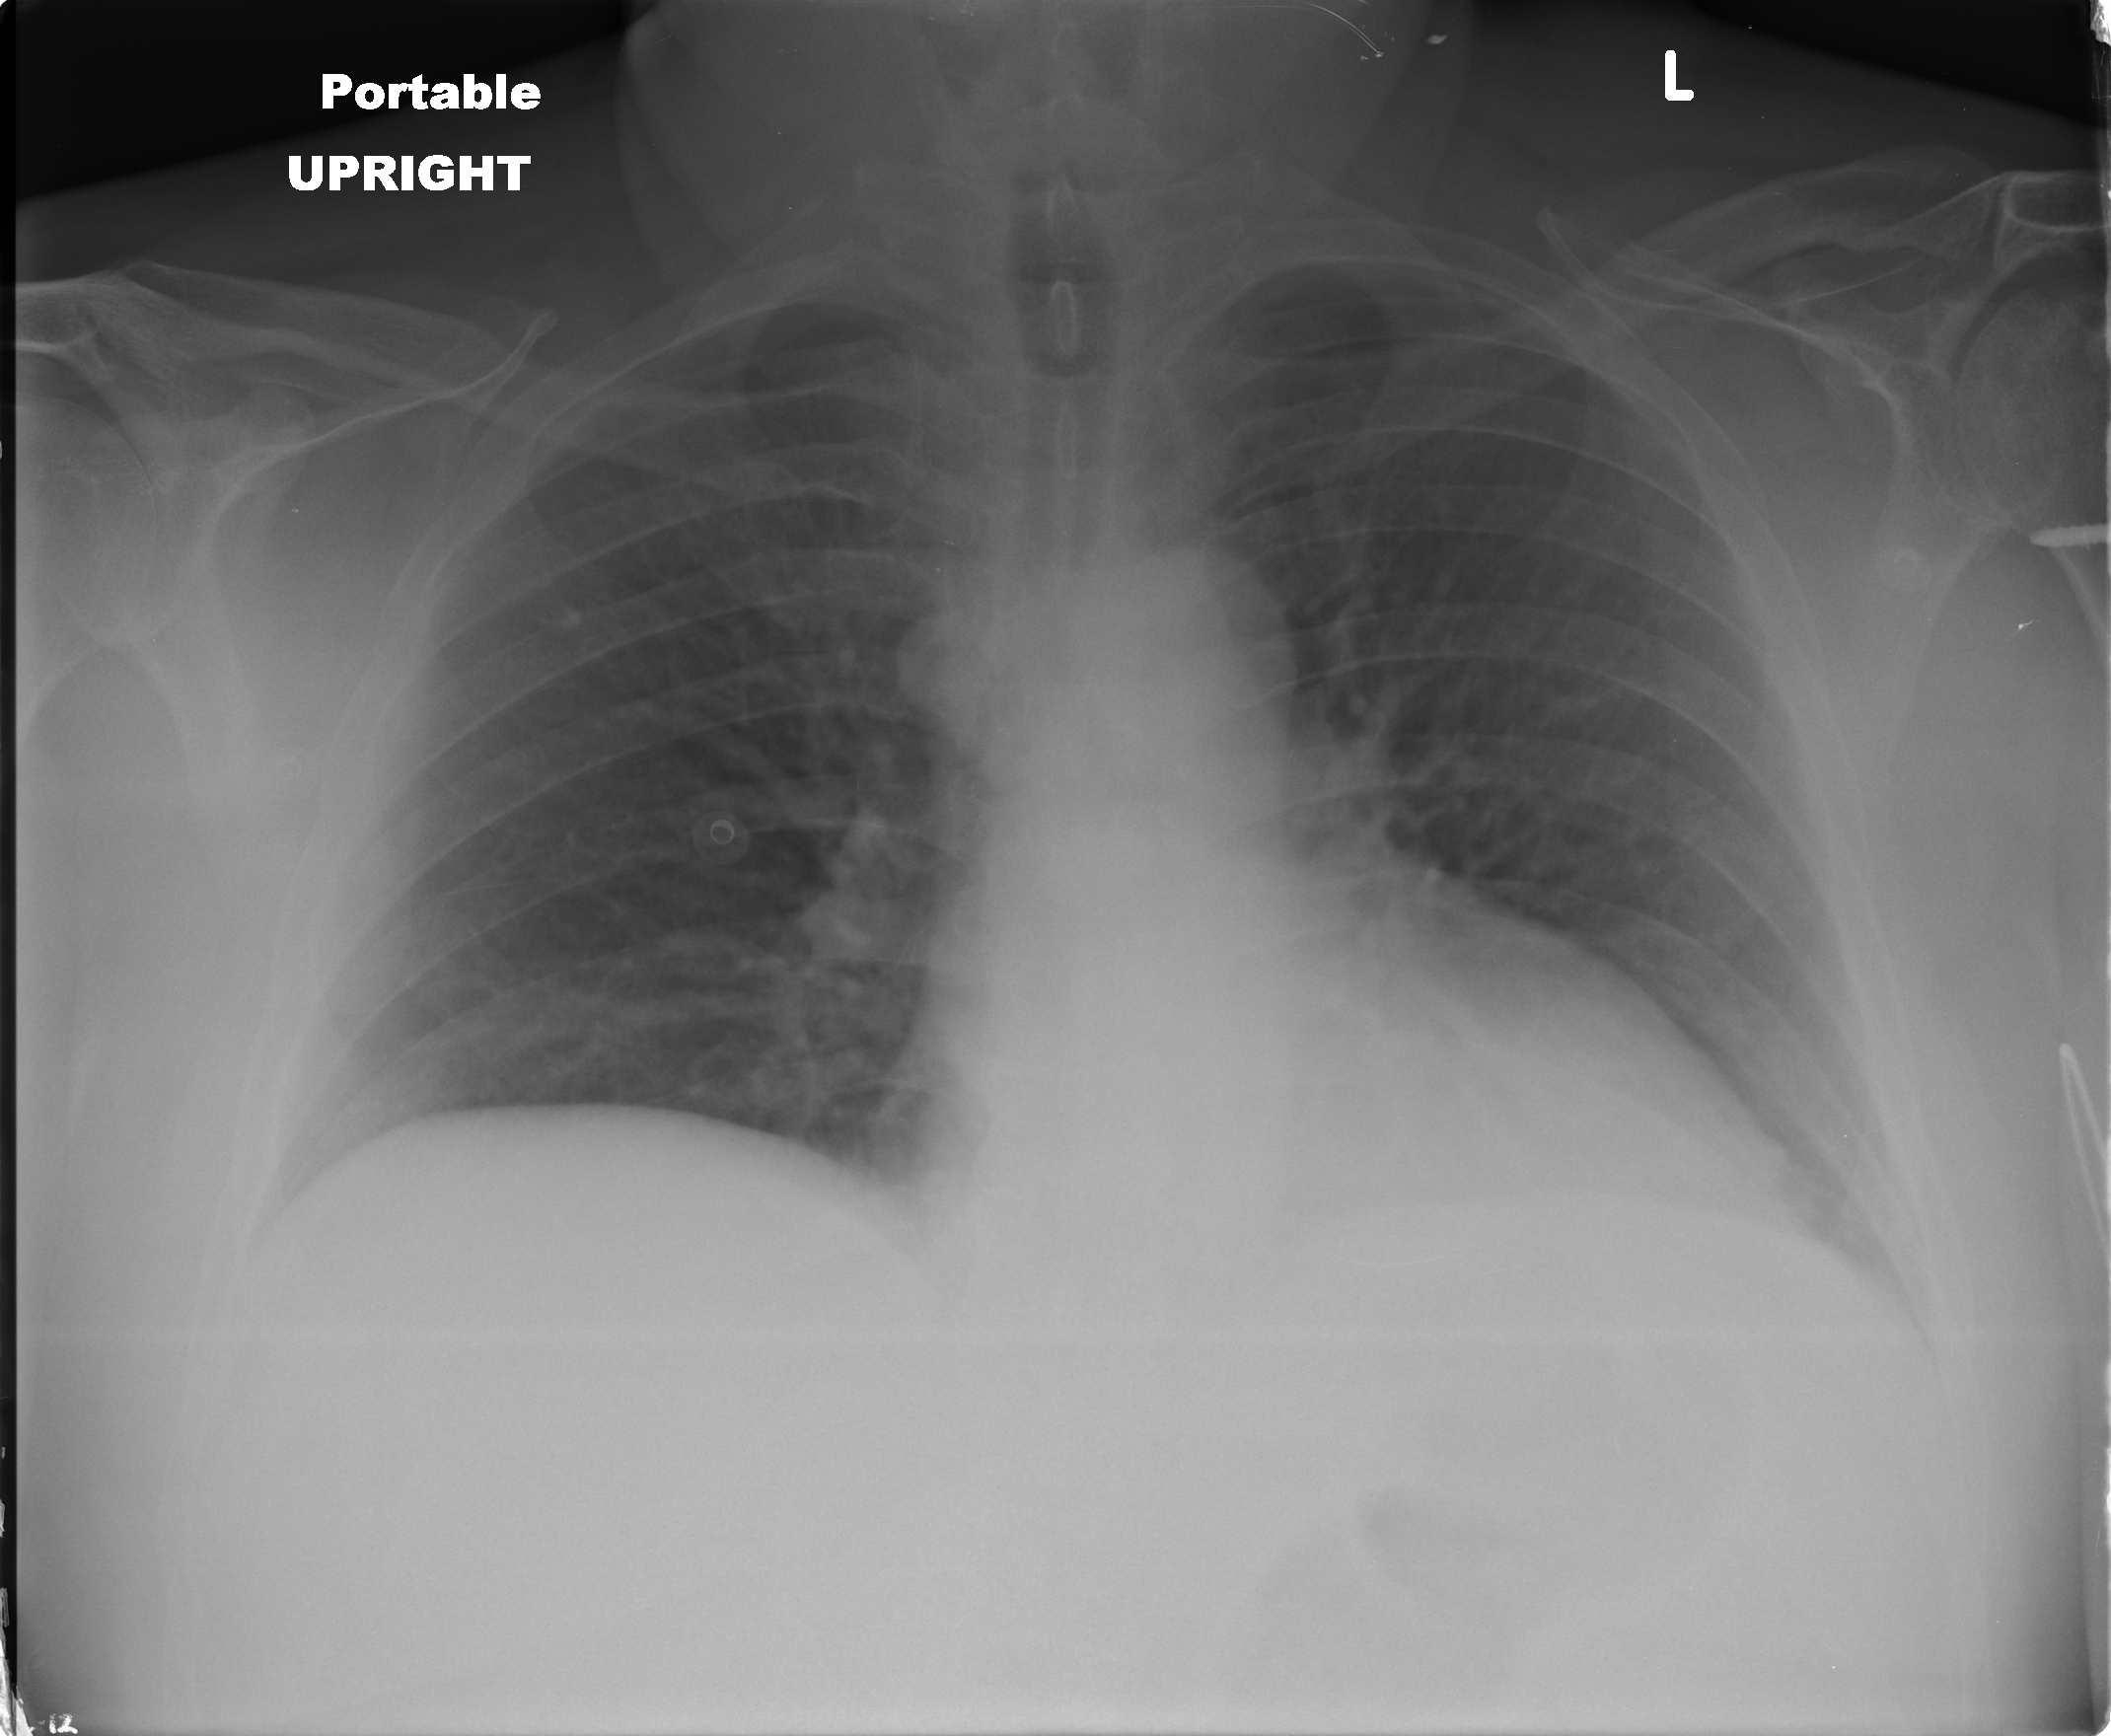
Portable chest radiograph, AP projection. Male patient, age 56 years; imaged 0 days after the COVID-19 diagnosis.
Key findings recorded by the radiologist: lungs appear clear with no nodule, airspace consolidation or pleural effusion.